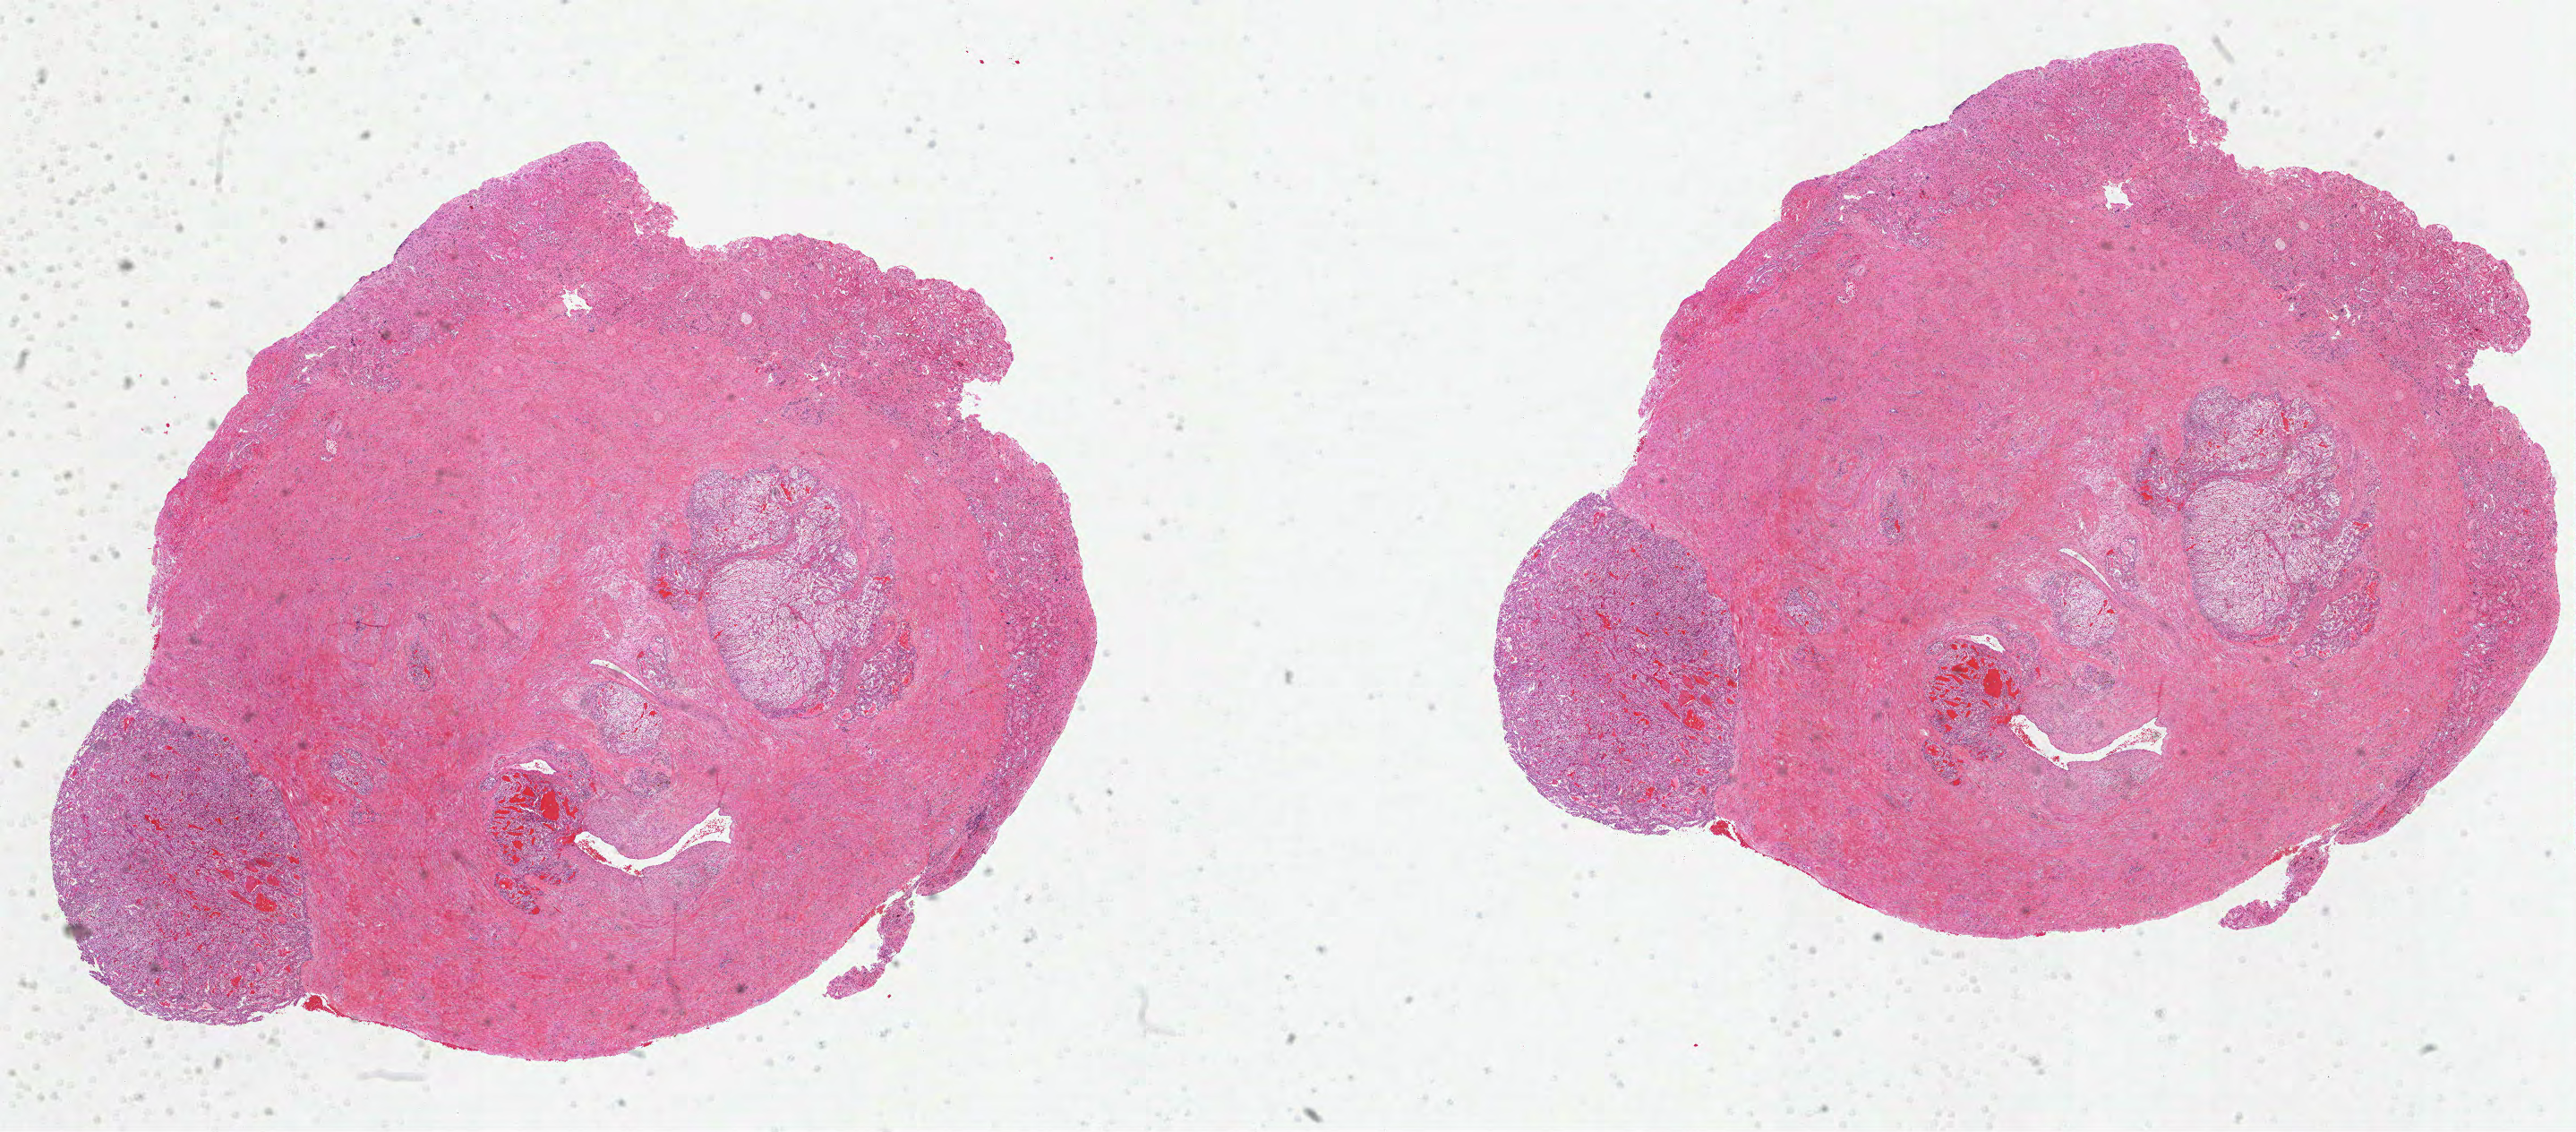
Whole-slide histology image, H&E-stained — whole scanned area (about 23.2 x 10.2 mm, from a 40x scan) shown as a low-resolution overview, FFPE section, sample: primary tumour, kidney. Female patient; age at initial diagnosis 40 years. Histologic grade: G2 (moderately differentiated).
- AJCC pathologic stage: I
- pathologic diagnosis: Clear cell adenocarcinoma, NOS